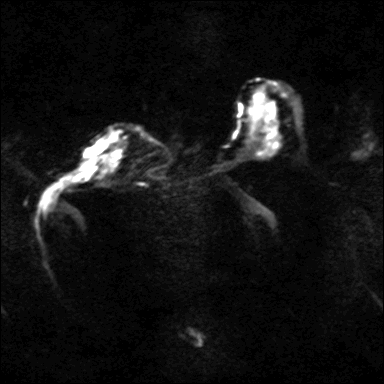
Breast MRI, one axial slice; slice 25 of 40 in the series (ordered by position); diffusion-weighted series; image 2 of 4 stored at this slice position (different b-values; order by instance number); 3 T; 4.2 mm slice thickness; 384 × 384 image matrix, field of view 320 × 320 mm. Female patient.
Outlined on this slice (expert manual segmentation):
- tumour on diffusion-weighted imaging: box from (x=86, y=135) to (x=115, y=153) px